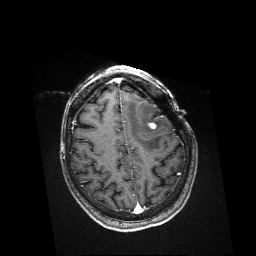
Brain MRI from a brain-tumour surgery series, one axial slice. Position 127 of 176 along the scan axis. T1-weighted post-contrast. 256 × 256 image matrix, field of view 256 × 256 mm. From the clinical record (not read from this slice): histopathology: Metastatic Melanoma; tumour location: Left Frontal.
Structures marked on this image (expert manual segmentation):
- residual tumour: bounding box (x1, y1, x2, y2) in pixels: (147, 122, 157, 130)